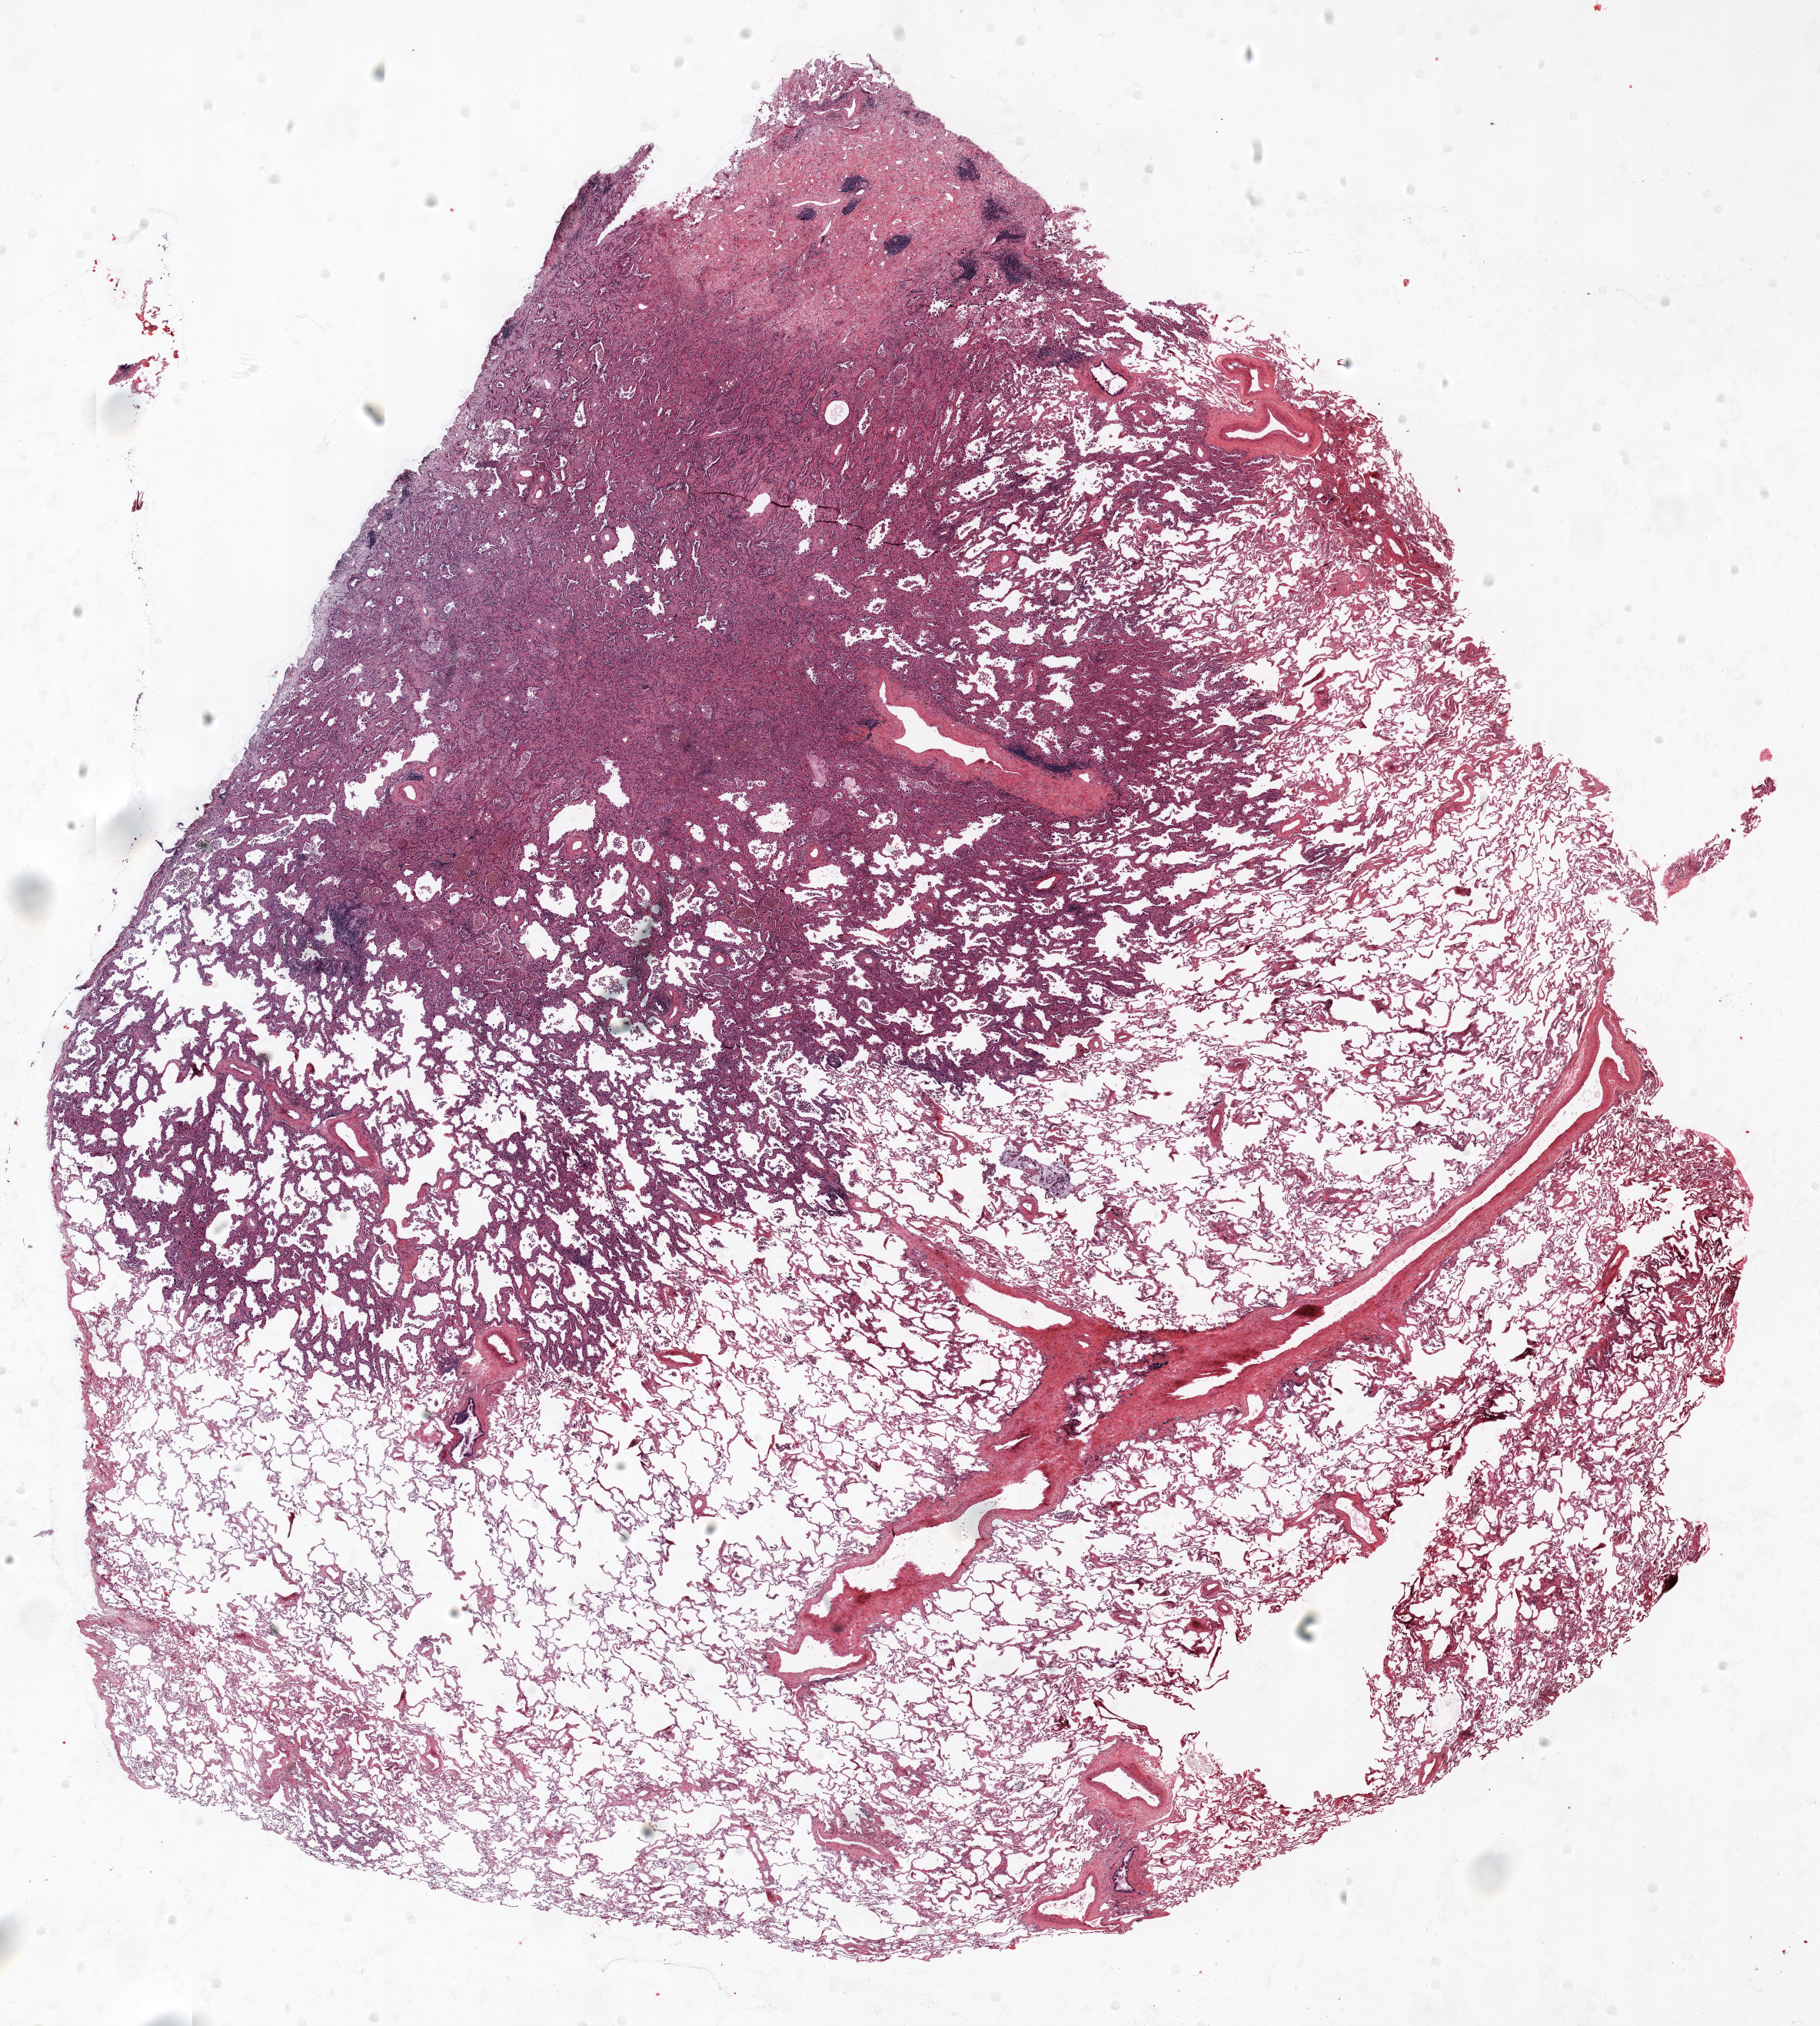
Whole-slide histology image, H&E, low-resolution overview of the scanned area, about 19.0 x 21.2 mm; FFPE section; lung. Female, age 56 at enrolment. Current smoker at enrolment. Grade: well differentiated (G1).
Tumour size (pathology): 15 mm. Participant's lung-cancer diagnosis: Bronchiolo-alveolar adenocarcinoma, NOS (ICD-O-3 8250/3). Primary tumour location (clinical record): right upper lobe. Stage (AJCC 6th edition): IA.